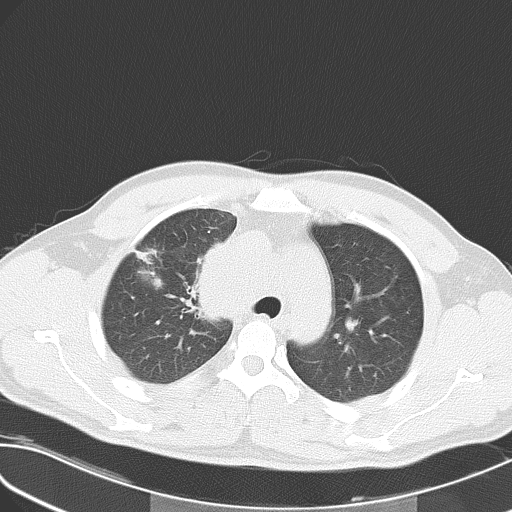
Chest CT, one axial slice. Slice 41 of 55 in the series (ordered by position). Reconstruction kernel B70f. 120 kVp. Lung window (W 1500 / L -600 HU). 512 × 512 image matrix. Male patient, age 32 years. From the clinical record (not read from this slice): clinical TNM (as recorded): T4 N3 M0; histopathological grade: G3.
Structures marked on this image (rectangle marked by the reading radiologist):
- lung tumour (recorded histology: small cell carcinoma): bounding box [x1, y1, x2, y2] px = [176, 225, 247, 332]